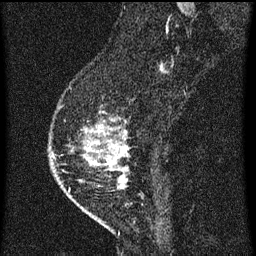
Breast MRI (dynamic contrast-enhanced), one sagittal slice. Slice 18 of 60 in the series (ordered by position). Dynamic contrast-enhanced series, image 2 of 3 at this slice position (ordered by acquisition). 1.5 T. TE 4.2 ms, TR 8 ms. 256 × 256 image matrix. Patient: female, 47 years.
Outlined on this slice (semi-automatically segmented with operator editing):
- analysis volume of interest (the breast-tissue region the enhancement analysis was run in; not a lesion): bounding box <50,88,132,203> (left, top, right, bottom; pixels)
- tumour enhancement mask (voxels above the 70 % enhancement threshold inside the analysis volume of interest): <53,128,129,187>